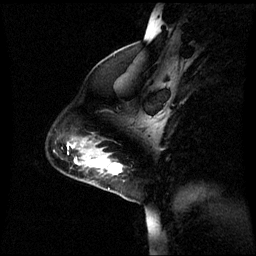
Breast MRI (dynamic contrast-enhanced), one sagittal slice; slice 16 of 60 in the series (ordered by position); dynamic contrast-enhanced series, image 2 of 3 at this slice position (ordered by acquisition); 1.5 T; TE 4.2 ms, TR 8.9 ms; 2.2 mm slice thickness; 256 × 256 image matrix, field of view 240 × 240 mm. Patient: female, 44 years. Case-level facts recorded for this patient, not image findings: setting: breast cancer imaged before/during neoadjuvant chemotherapy; receptor status: triple-negative.
Structures marked on this image (semi-automatic segmentation, software-assisted and operator-edited):
- analysis volume of interest (the breast-tissue region the enhancement analysis was run in; not a lesion): bounding box [x1, y1, x2, y2] px = [76, 150, 125, 185]
- tumour enhancement mask (voxels above the 70 % enhancement threshold inside the analysis volume of interest): [76, 160, 122, 175]